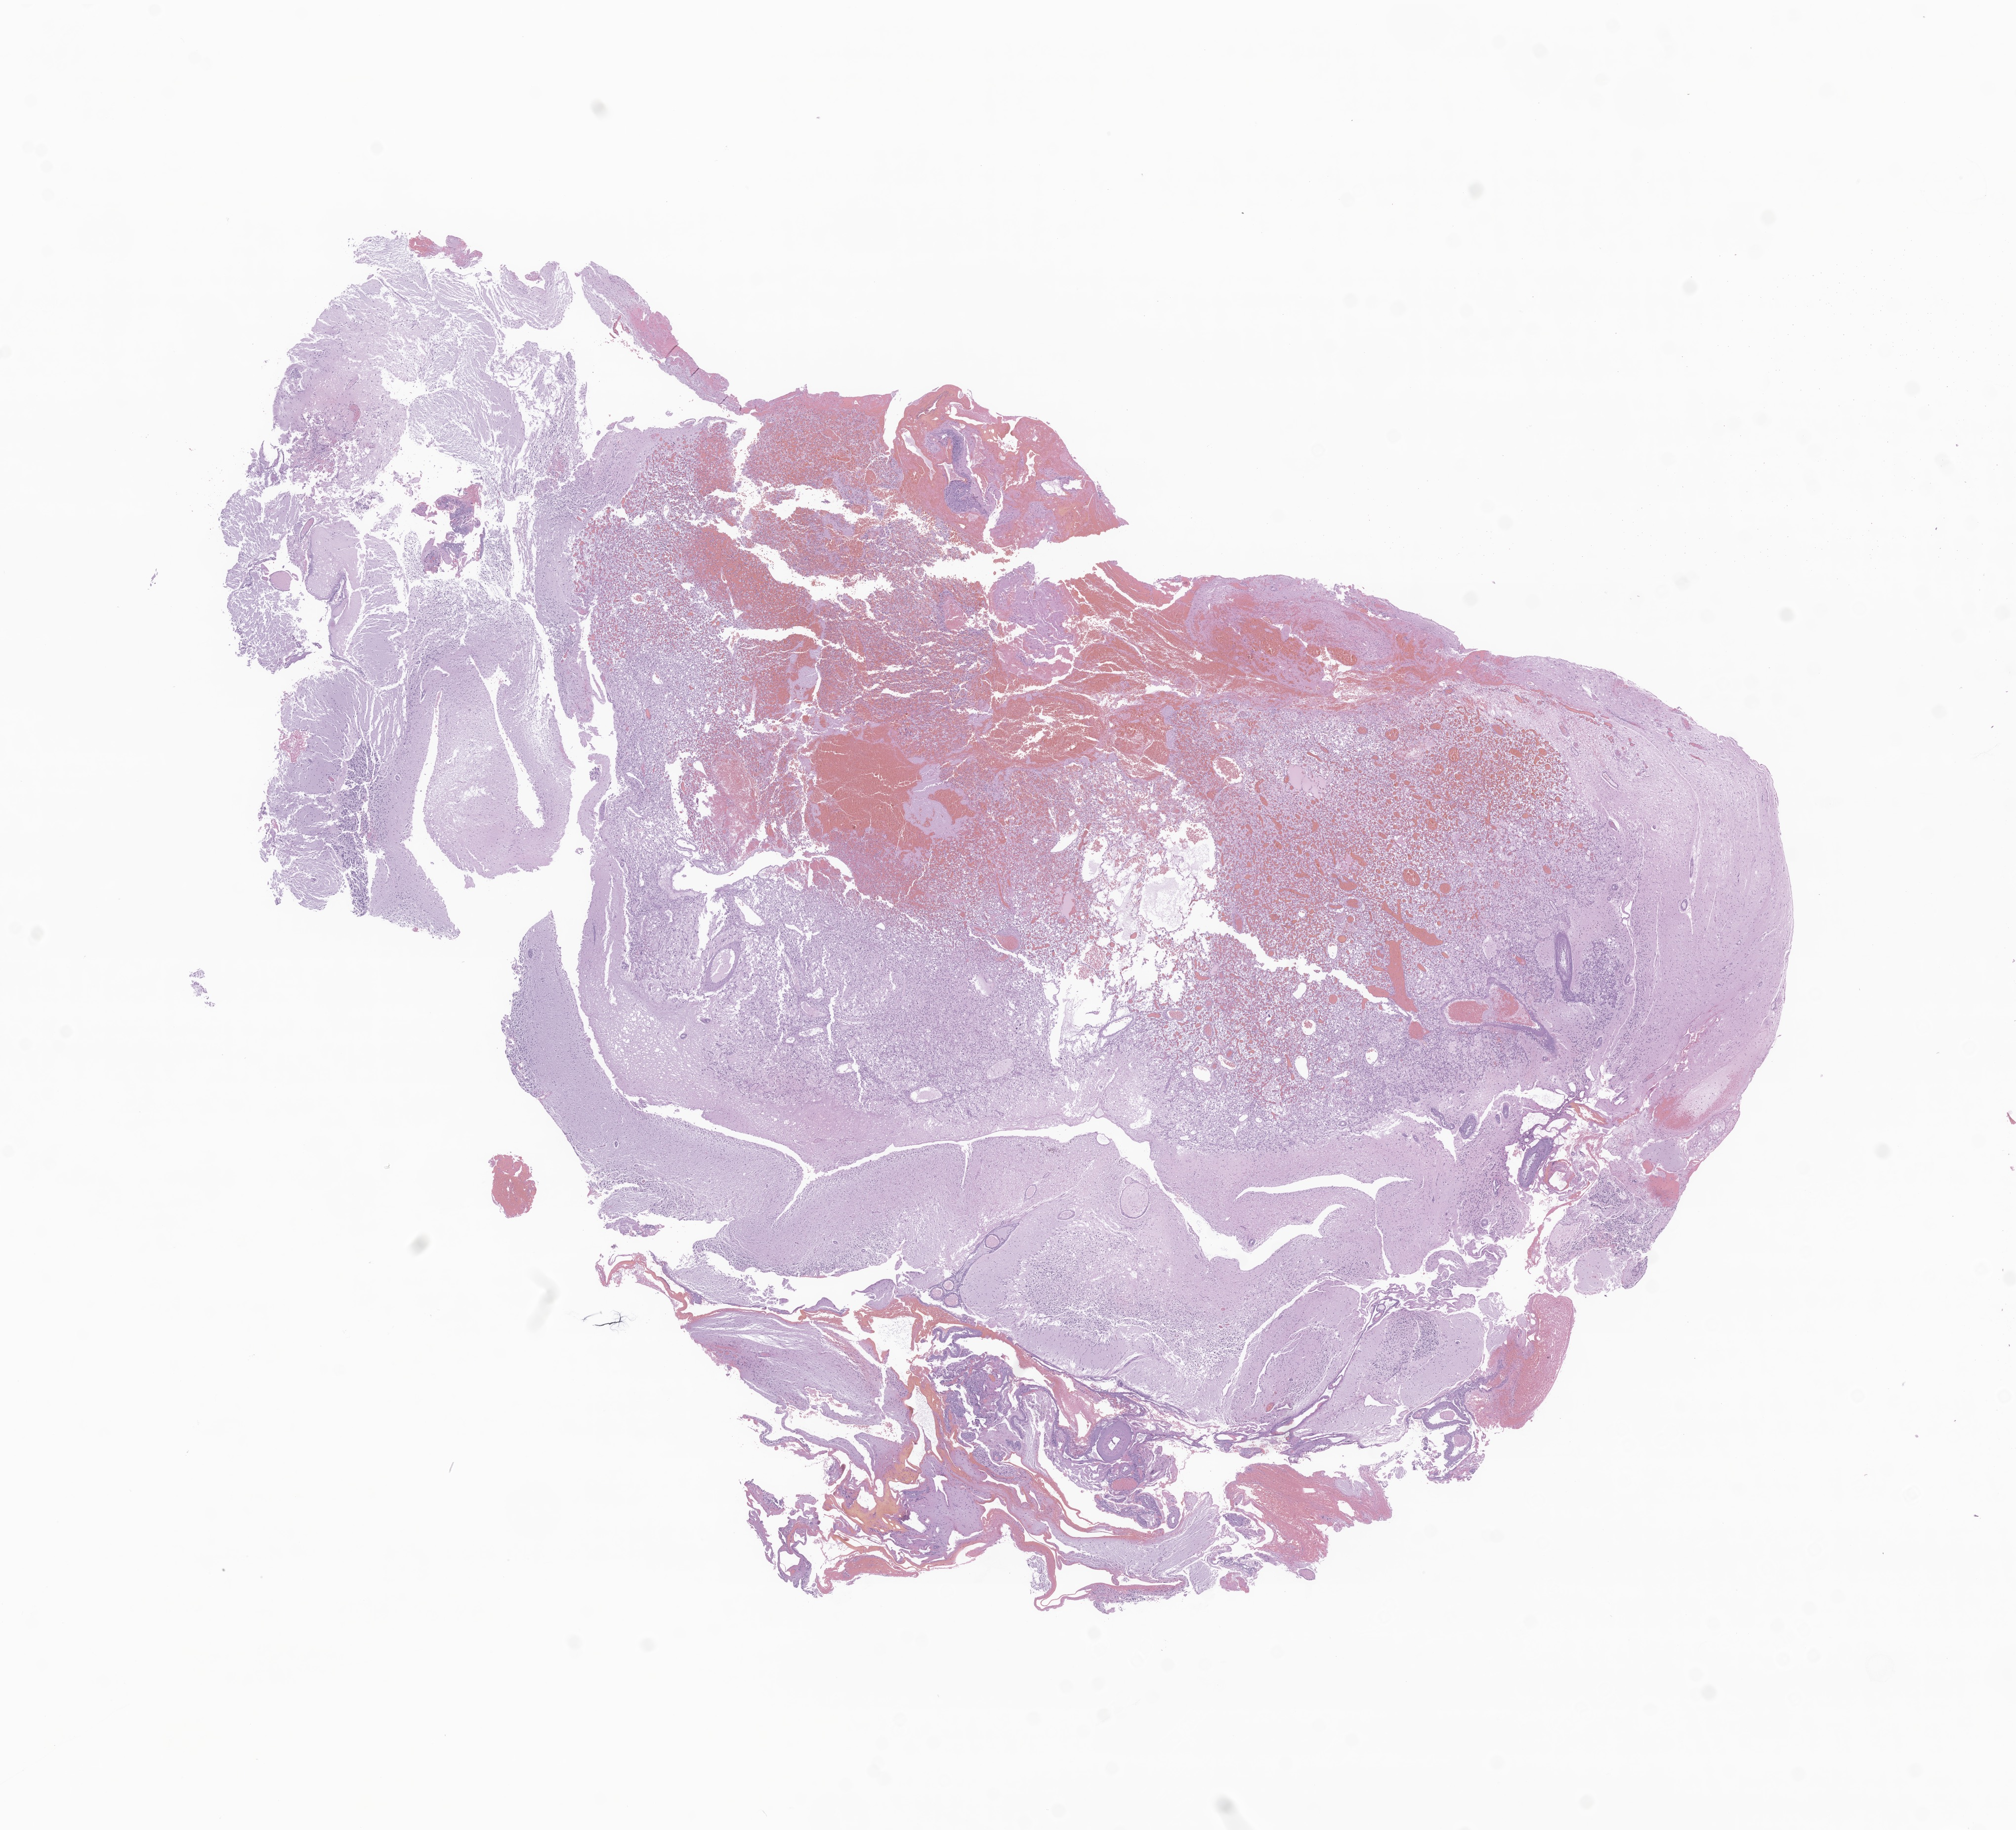
Digitized haematoxylin and eosin-stained section of tumor tissue from the brain — whole scanned area (about 17.2 x 15.6 mm) shown as a low-resolution overview; FFPE section. Female patient, age 179 months (14 years 11 months).
Diagnosis (ICD-O-3 morphology term): Neoplasm, malignant.